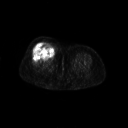
FDG PET of an extremity soft-tissue mass (from a PET/CT study), one axial slice. 128 × 128 image matrix, field of view 700 × 700 mm. Patient: female, 56 years. From the clinical record (not read from this slice): histological type: malignant solitary fibrous tumor; grade: intermediate; site of the primary tumour: right thigh.
Annotated regions visible in this slice (expert contour drawn on MRI and transferred to this co-registered scan by the dataset authors):
- gross tumour volume including surrounding oedema: bounding box (x1, y1, x2, y2) in pixels: (33, 42, 56, 60)
- gross tumour volume (mass): (34, 42, 55, 59)